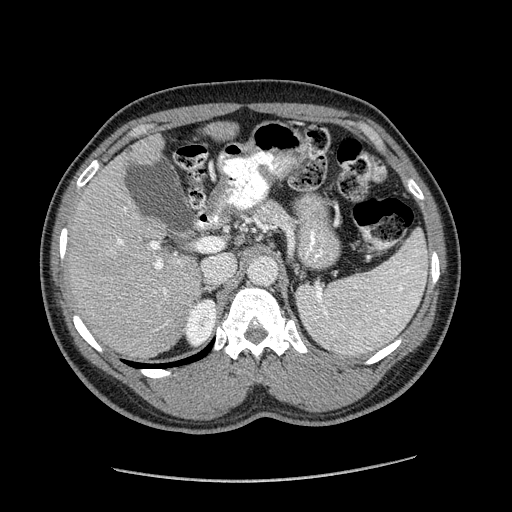
Contrast-enhanced abdominal CT (liver protocol), one axial slice. Slice 111 of 182 in the series (ordered by position). 120 kVp. Soft-tissue window (W 400 / L 40 HU). 2.5 mm slice thickness. 512 × 512 image matrix, field of view 400 × 400 mm. From the clinical record (not read from this slice): diagnosis: hepatocellular carcinoma (patient treated with transarterial chemoembolisation; whether this scan precedes or follows treatment is not stated here); TNM stage (as recorded): Stage-I; Child-Pugh class: A; tumour differentiation: well differentiated.
Structures marked on this image (semi-automatic segmentation, software-assisted and operator-edited):
- liver parenchyma outside the tumour (the mass and vessels are separate outlines, so this box may not span the whole liver): box from (x=66, y=122) to (x=238, y=358) px
- mass: (x=104, y=246)–(x=117, y=257)
- liver vessels: (x=117, y=207)–(x=180, y=328)